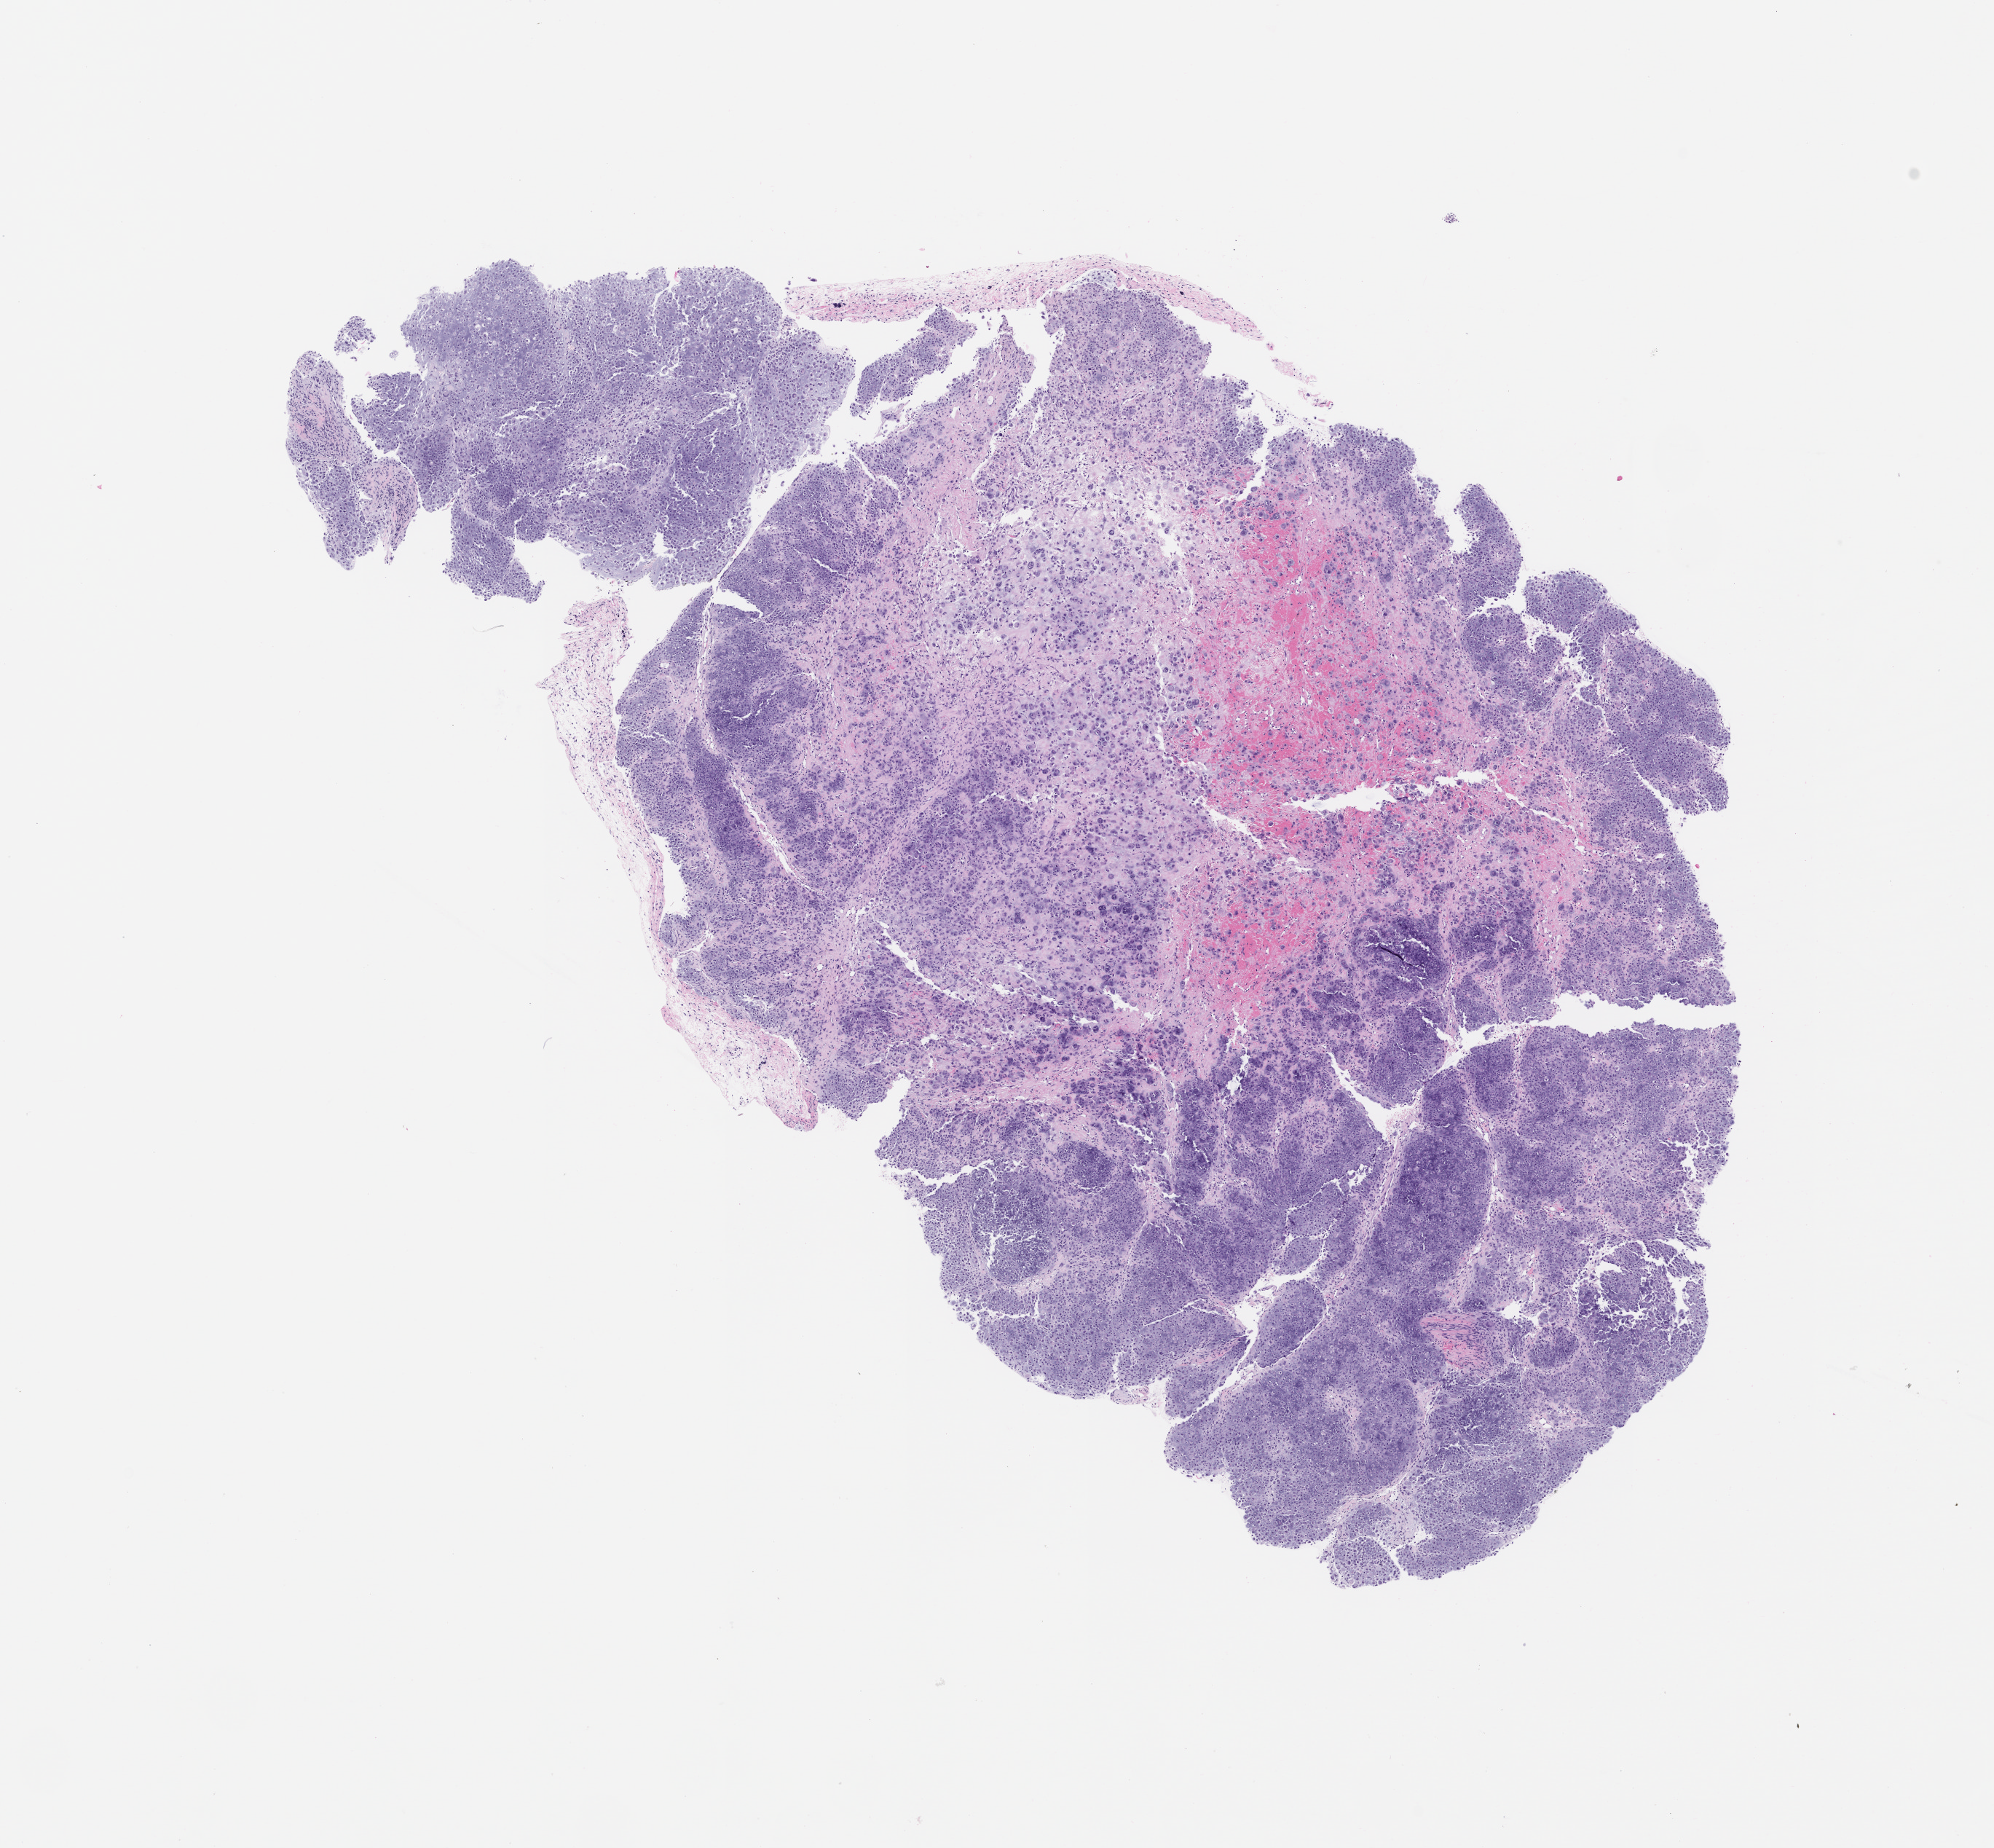
Whole-slide image, H&E: patient-derived xenograft (human tumor grown in a mouse), passage 1 — low-resolution overview of the scanned area, about 11.0 x 10.2 mm. Formalin-fixed, paraffin-embedded (FFPE) tissue. Tumor site category: musculoskeletal.
Originating patient diagnosis: Chondrosarcoma.